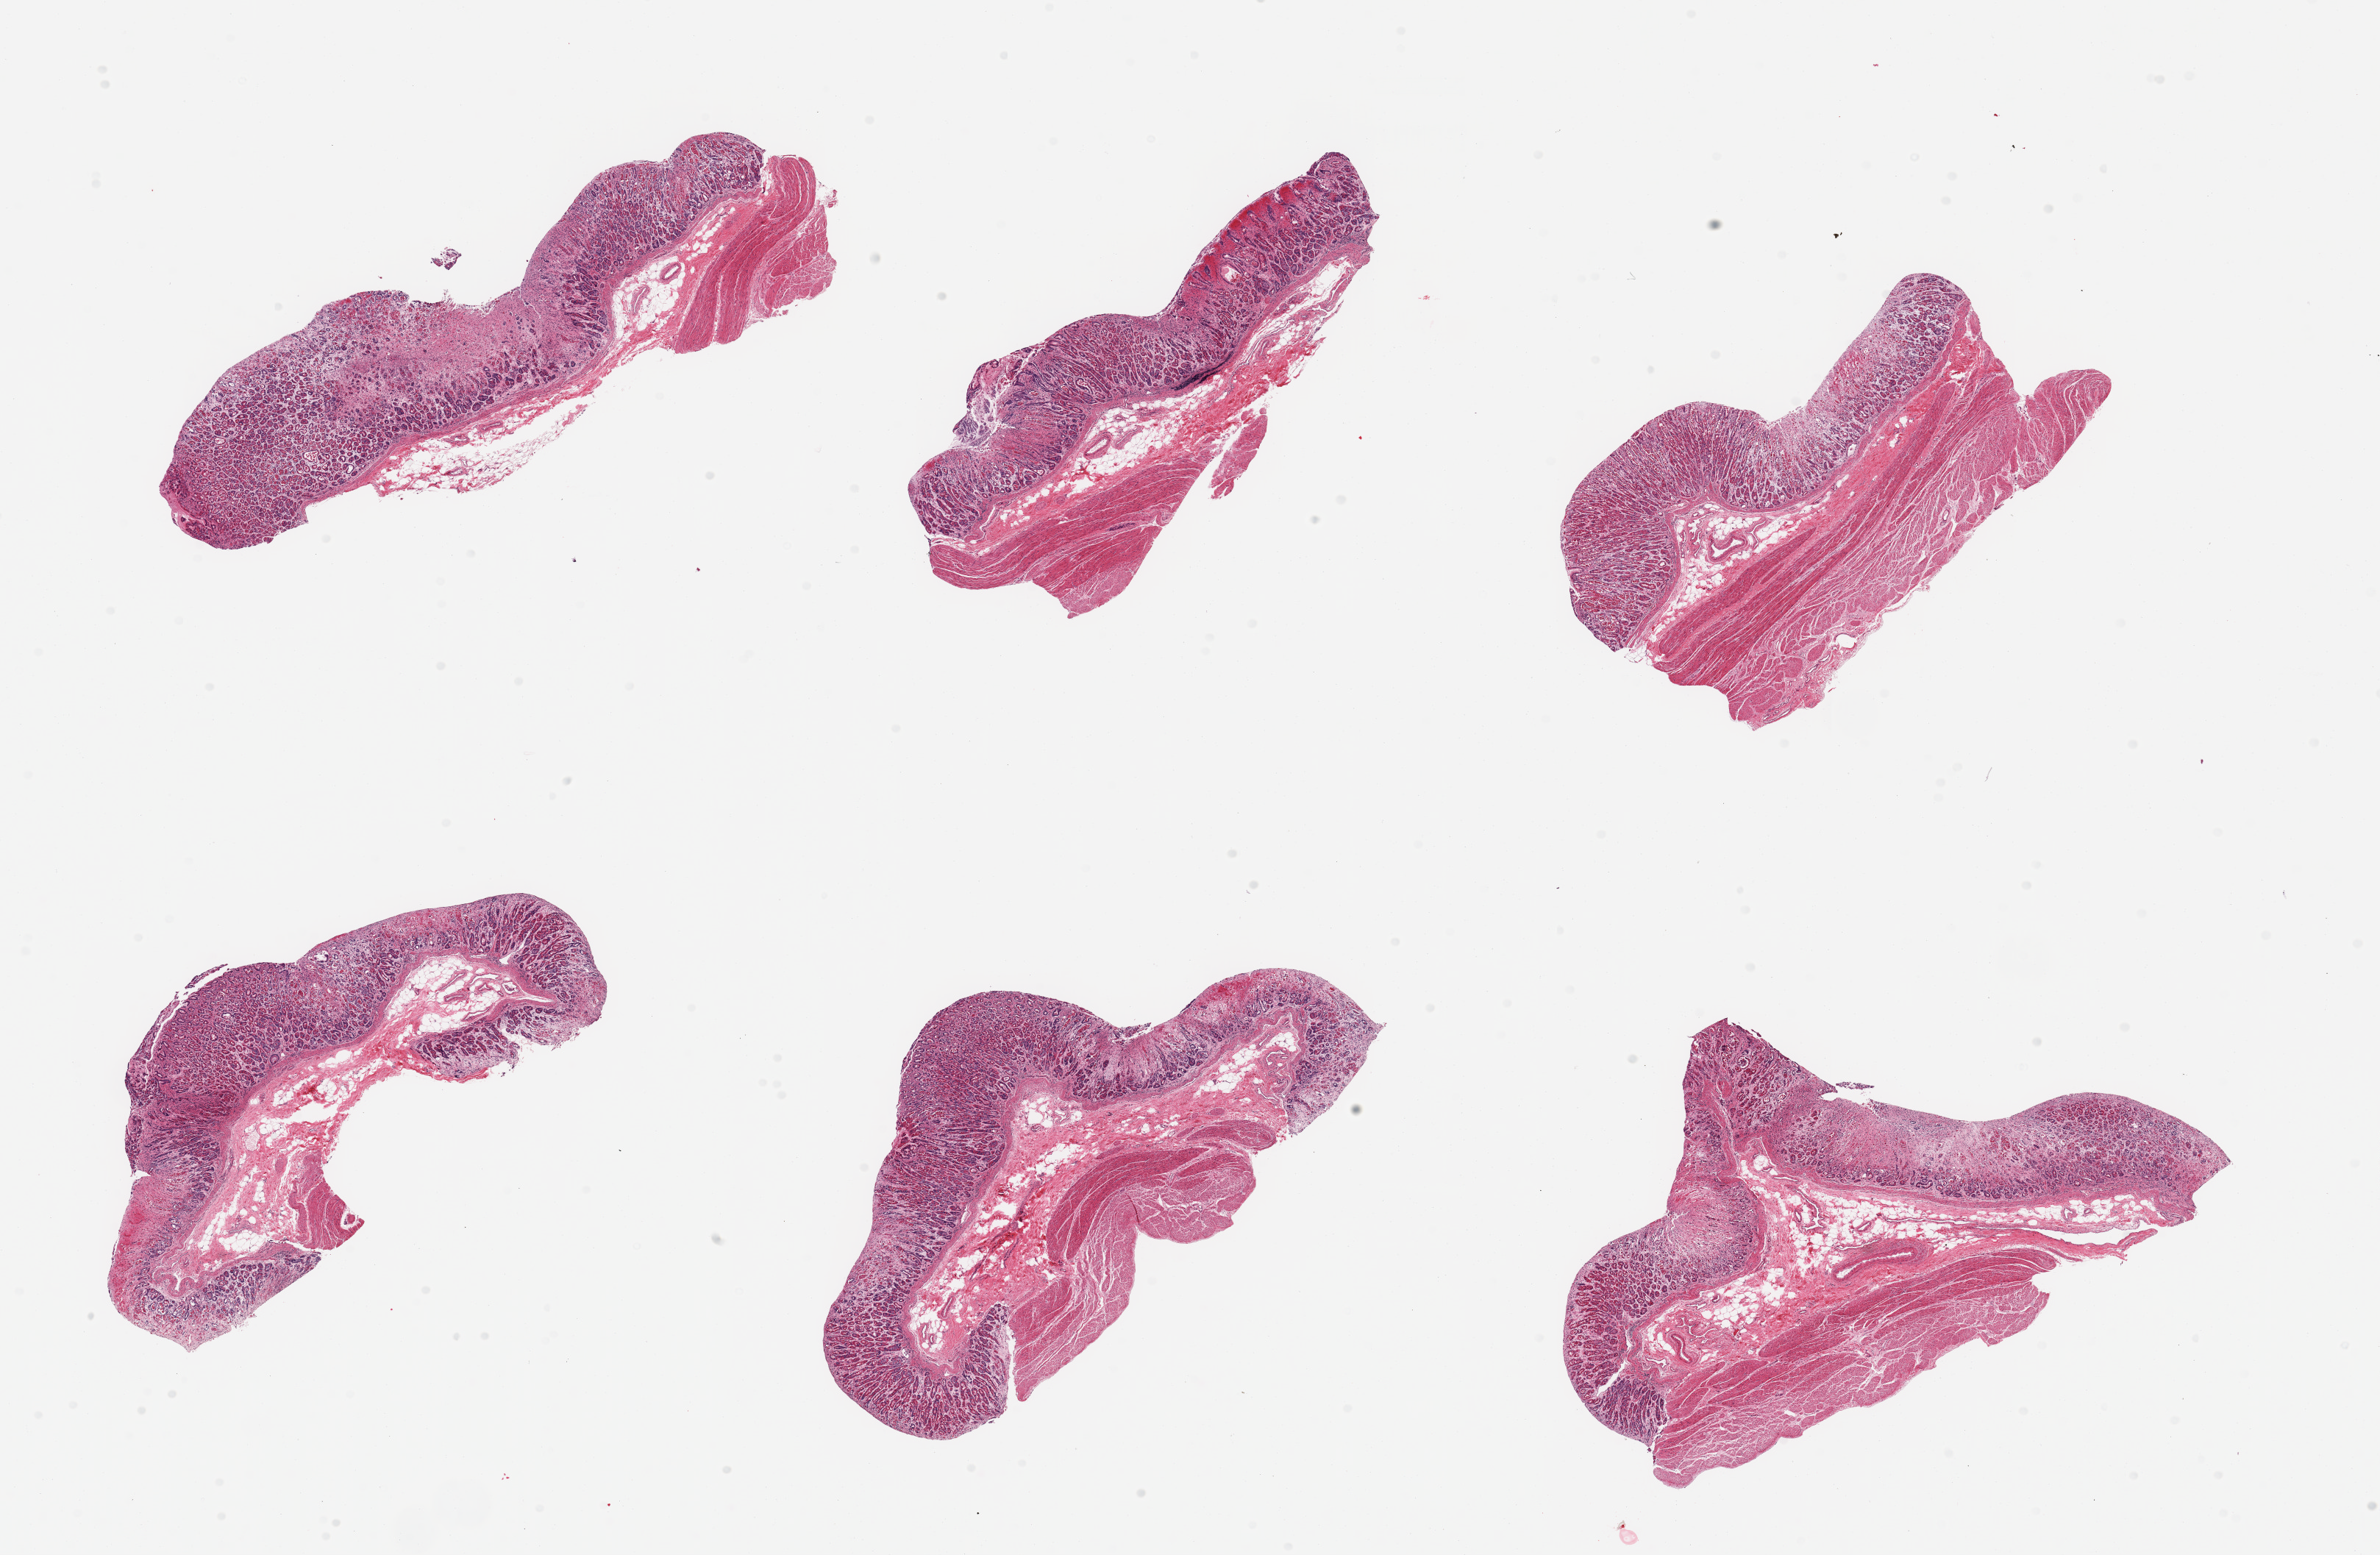
Hematoxylin and eosin (H&E) whole-slide image, whole scanned area (about 25.6 x 16.7 mm) shown as a low-resolution overview; PAXgene-fixed paraffin-embedded (PFPE) section; target tissue: stomach; donor tissue sample. Male donor.
Review note (as recorded): 6 pieces; portions of mucosa have severe autolysis.